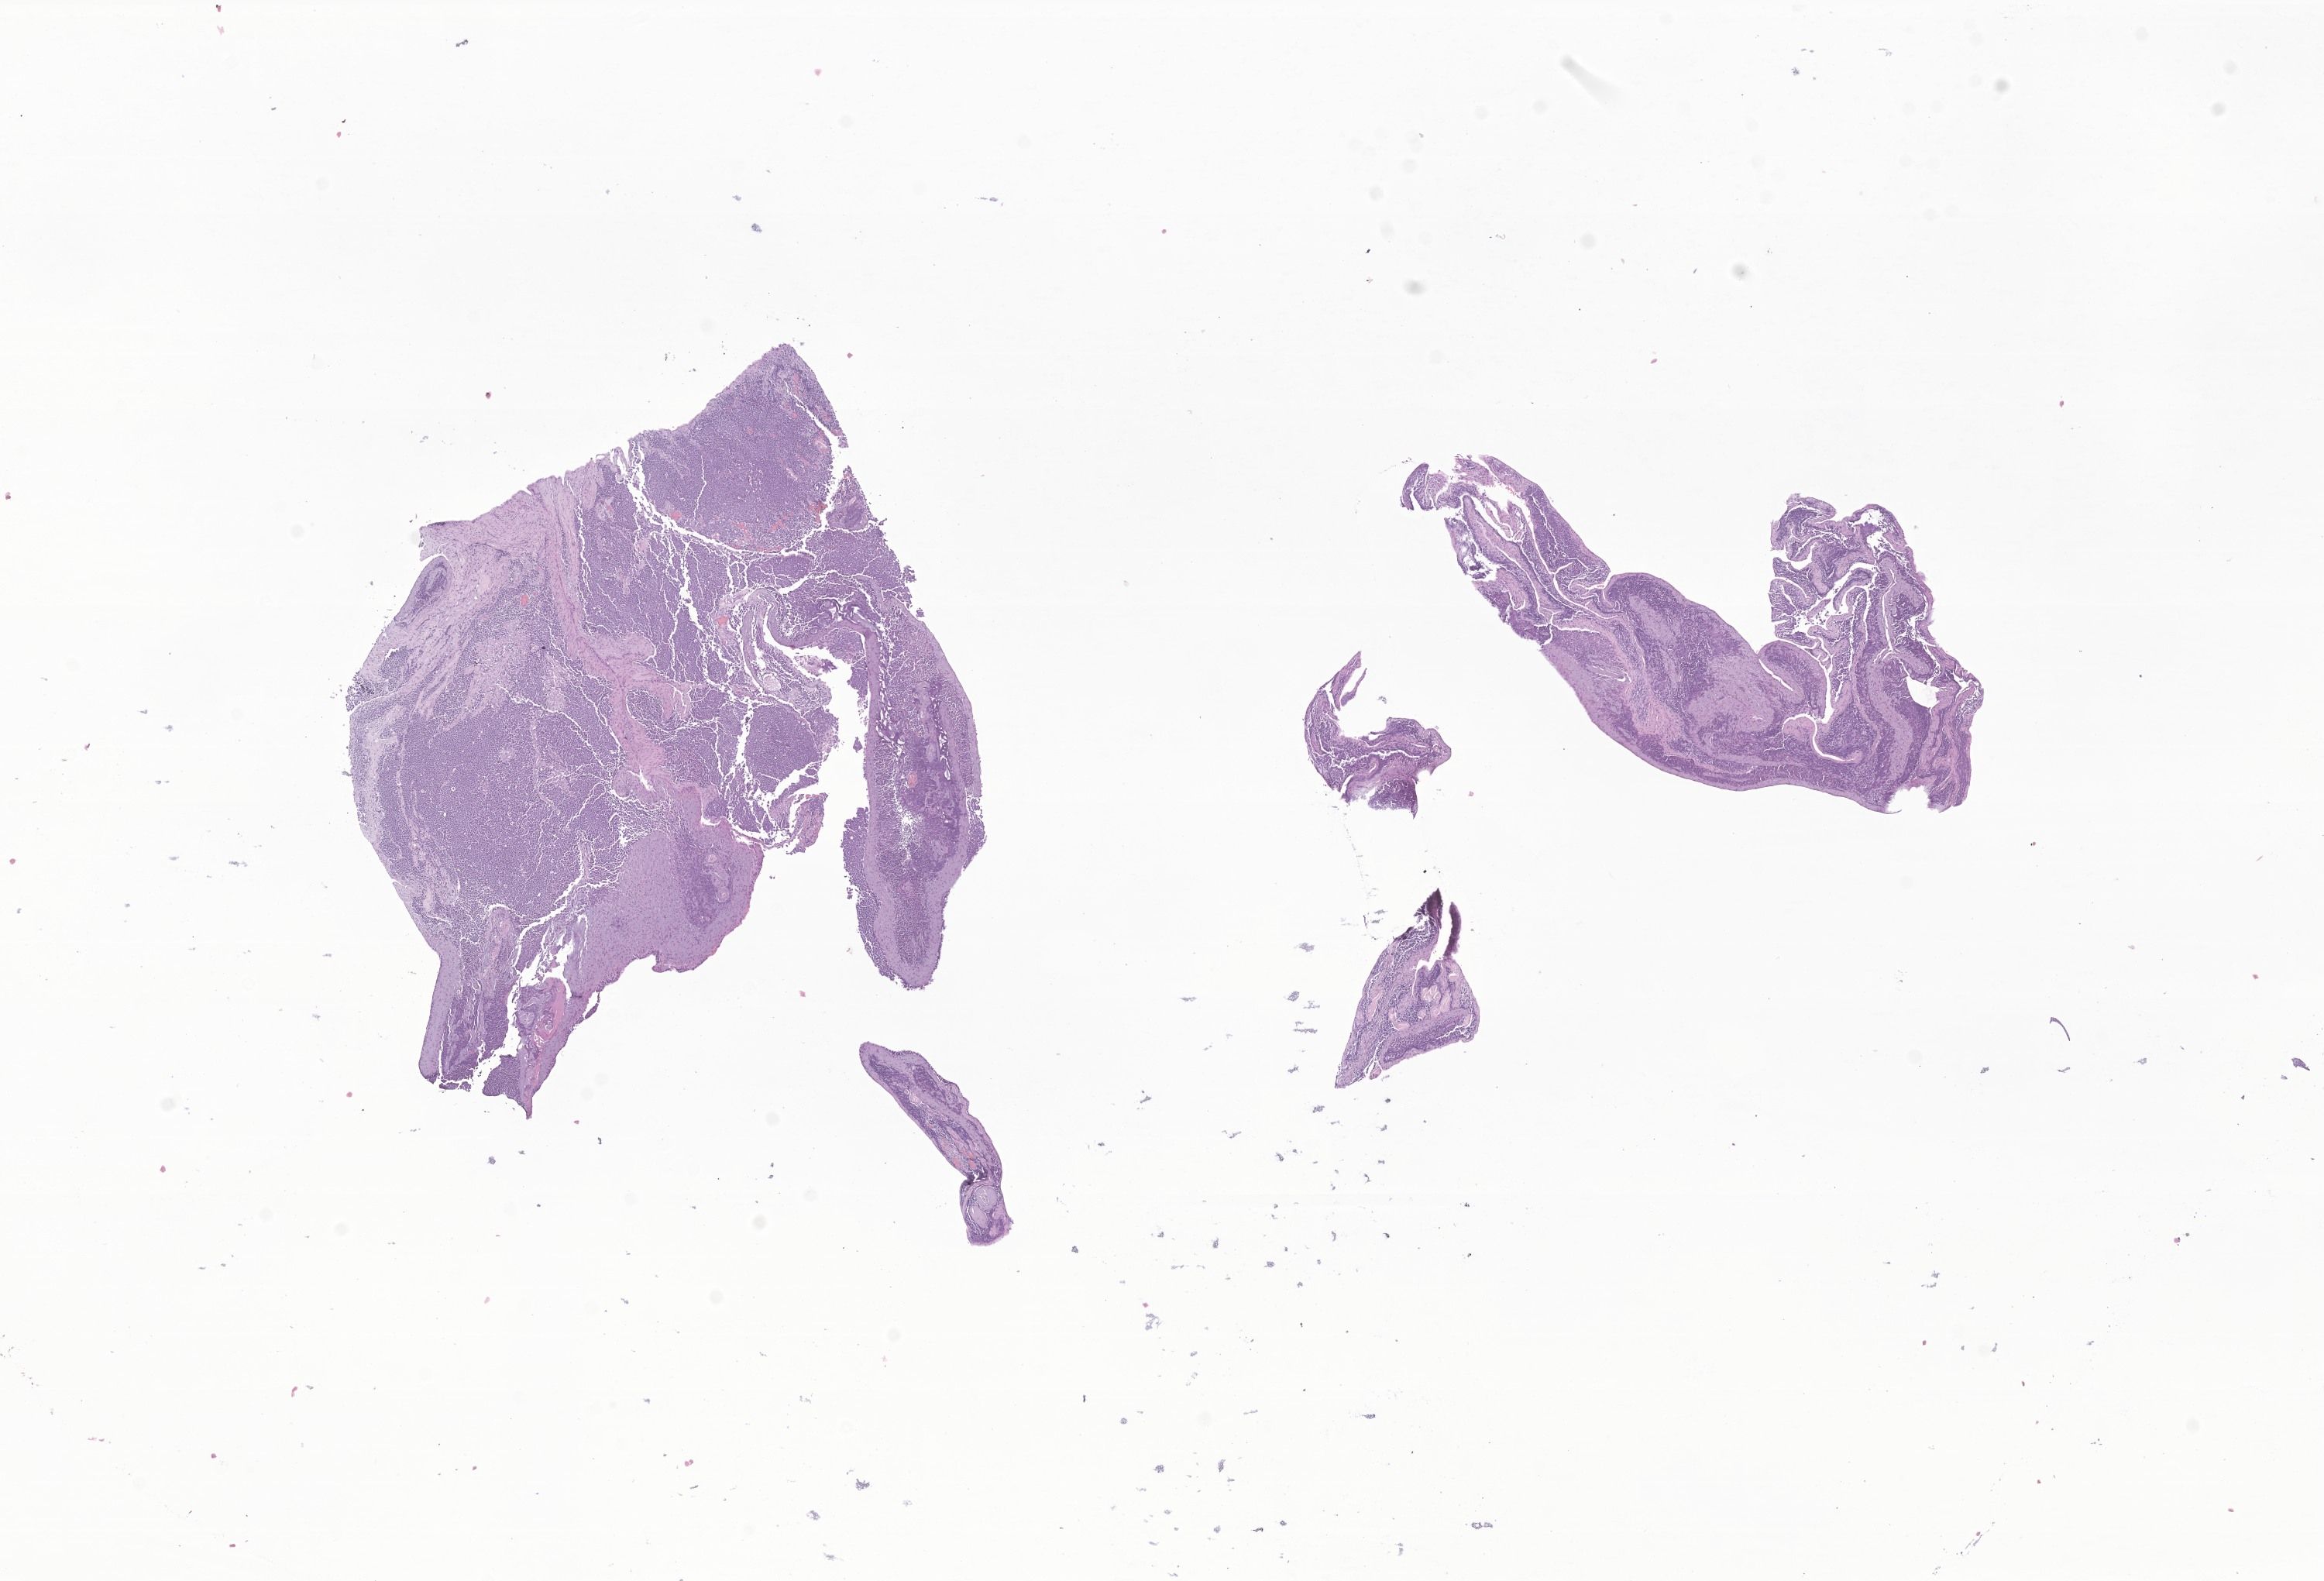
Whole-slide image, hematoxylin and eosin (H&E) stain of tumor tissue from the brain stem — a low-resolution overview of the entire scanned area, about 12.6 x 8.6 mm; formalin-fixed paraffin-embedded section. Patient male; age 142 months (11 years 10 months).
Recorded diagnosis: Medulloblastoma, NOS.